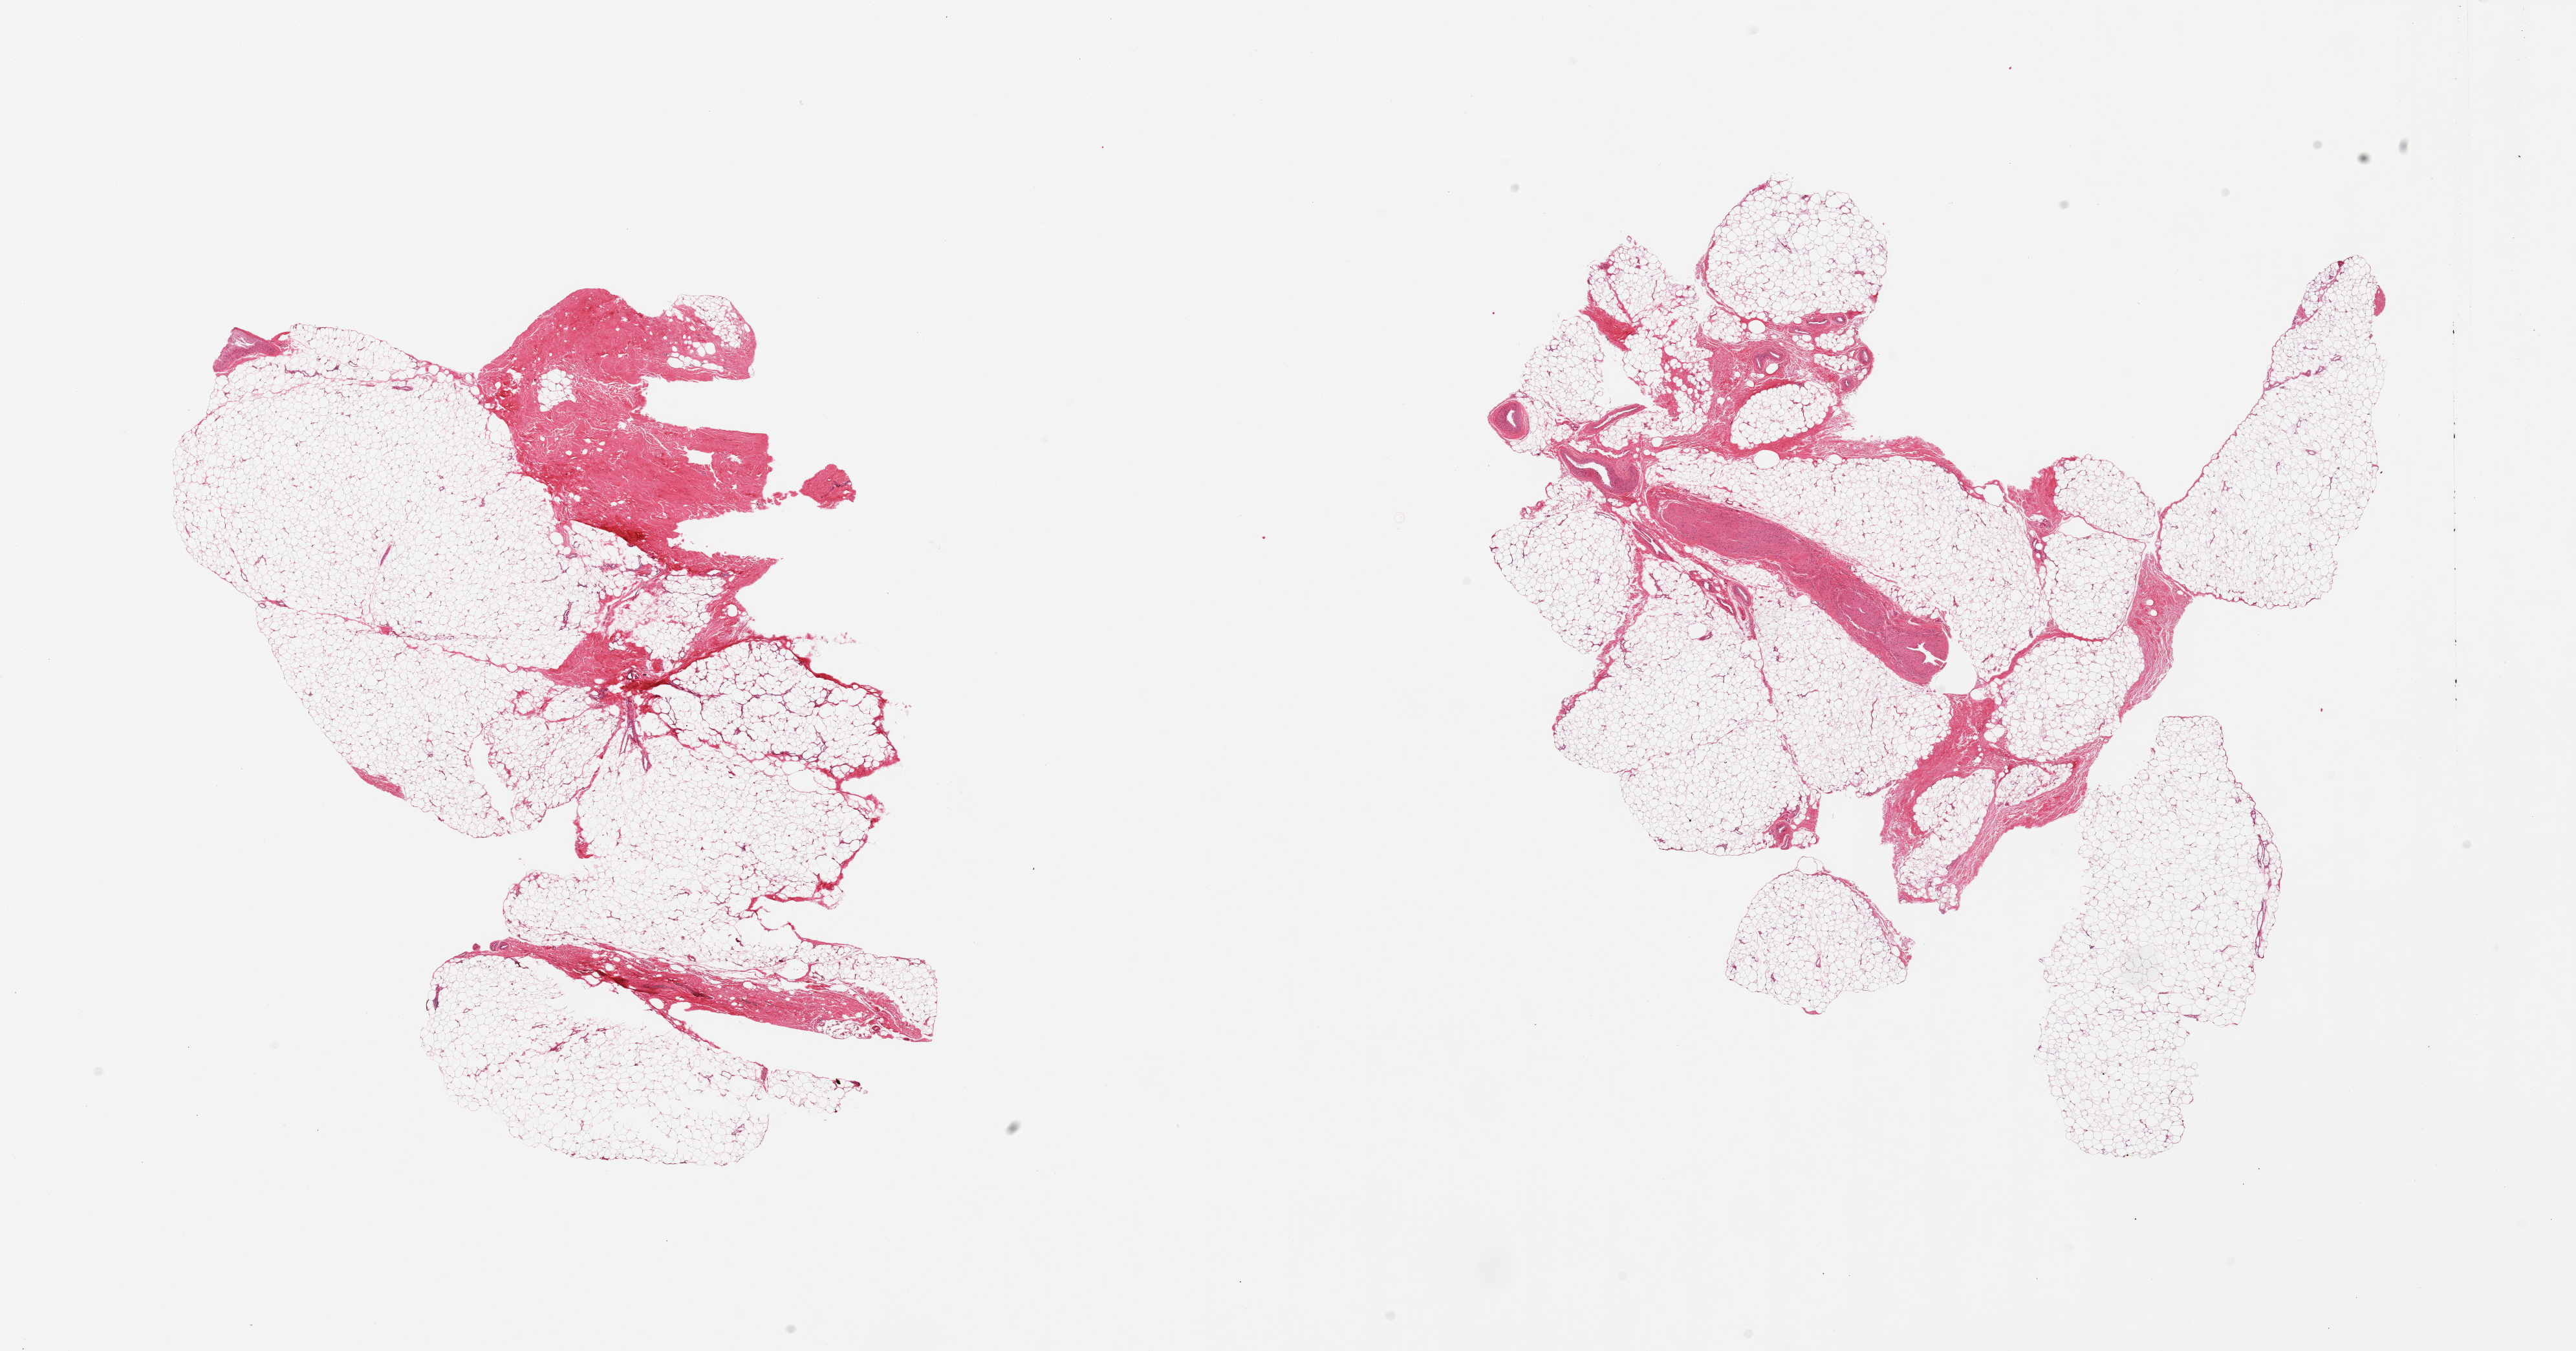
H&E whole-slide image — whole scanned area (about 31.5 x 16.5 mm) shown as a low-resolution overview; PAXgene-fixed paraffin-embedded (PFPE) section; target tissue: adipose tissue; tissue donor sample. Donor sex: male.
• reviewer comment on this tissue sample: 2 pieces; 10% fibrovascular content